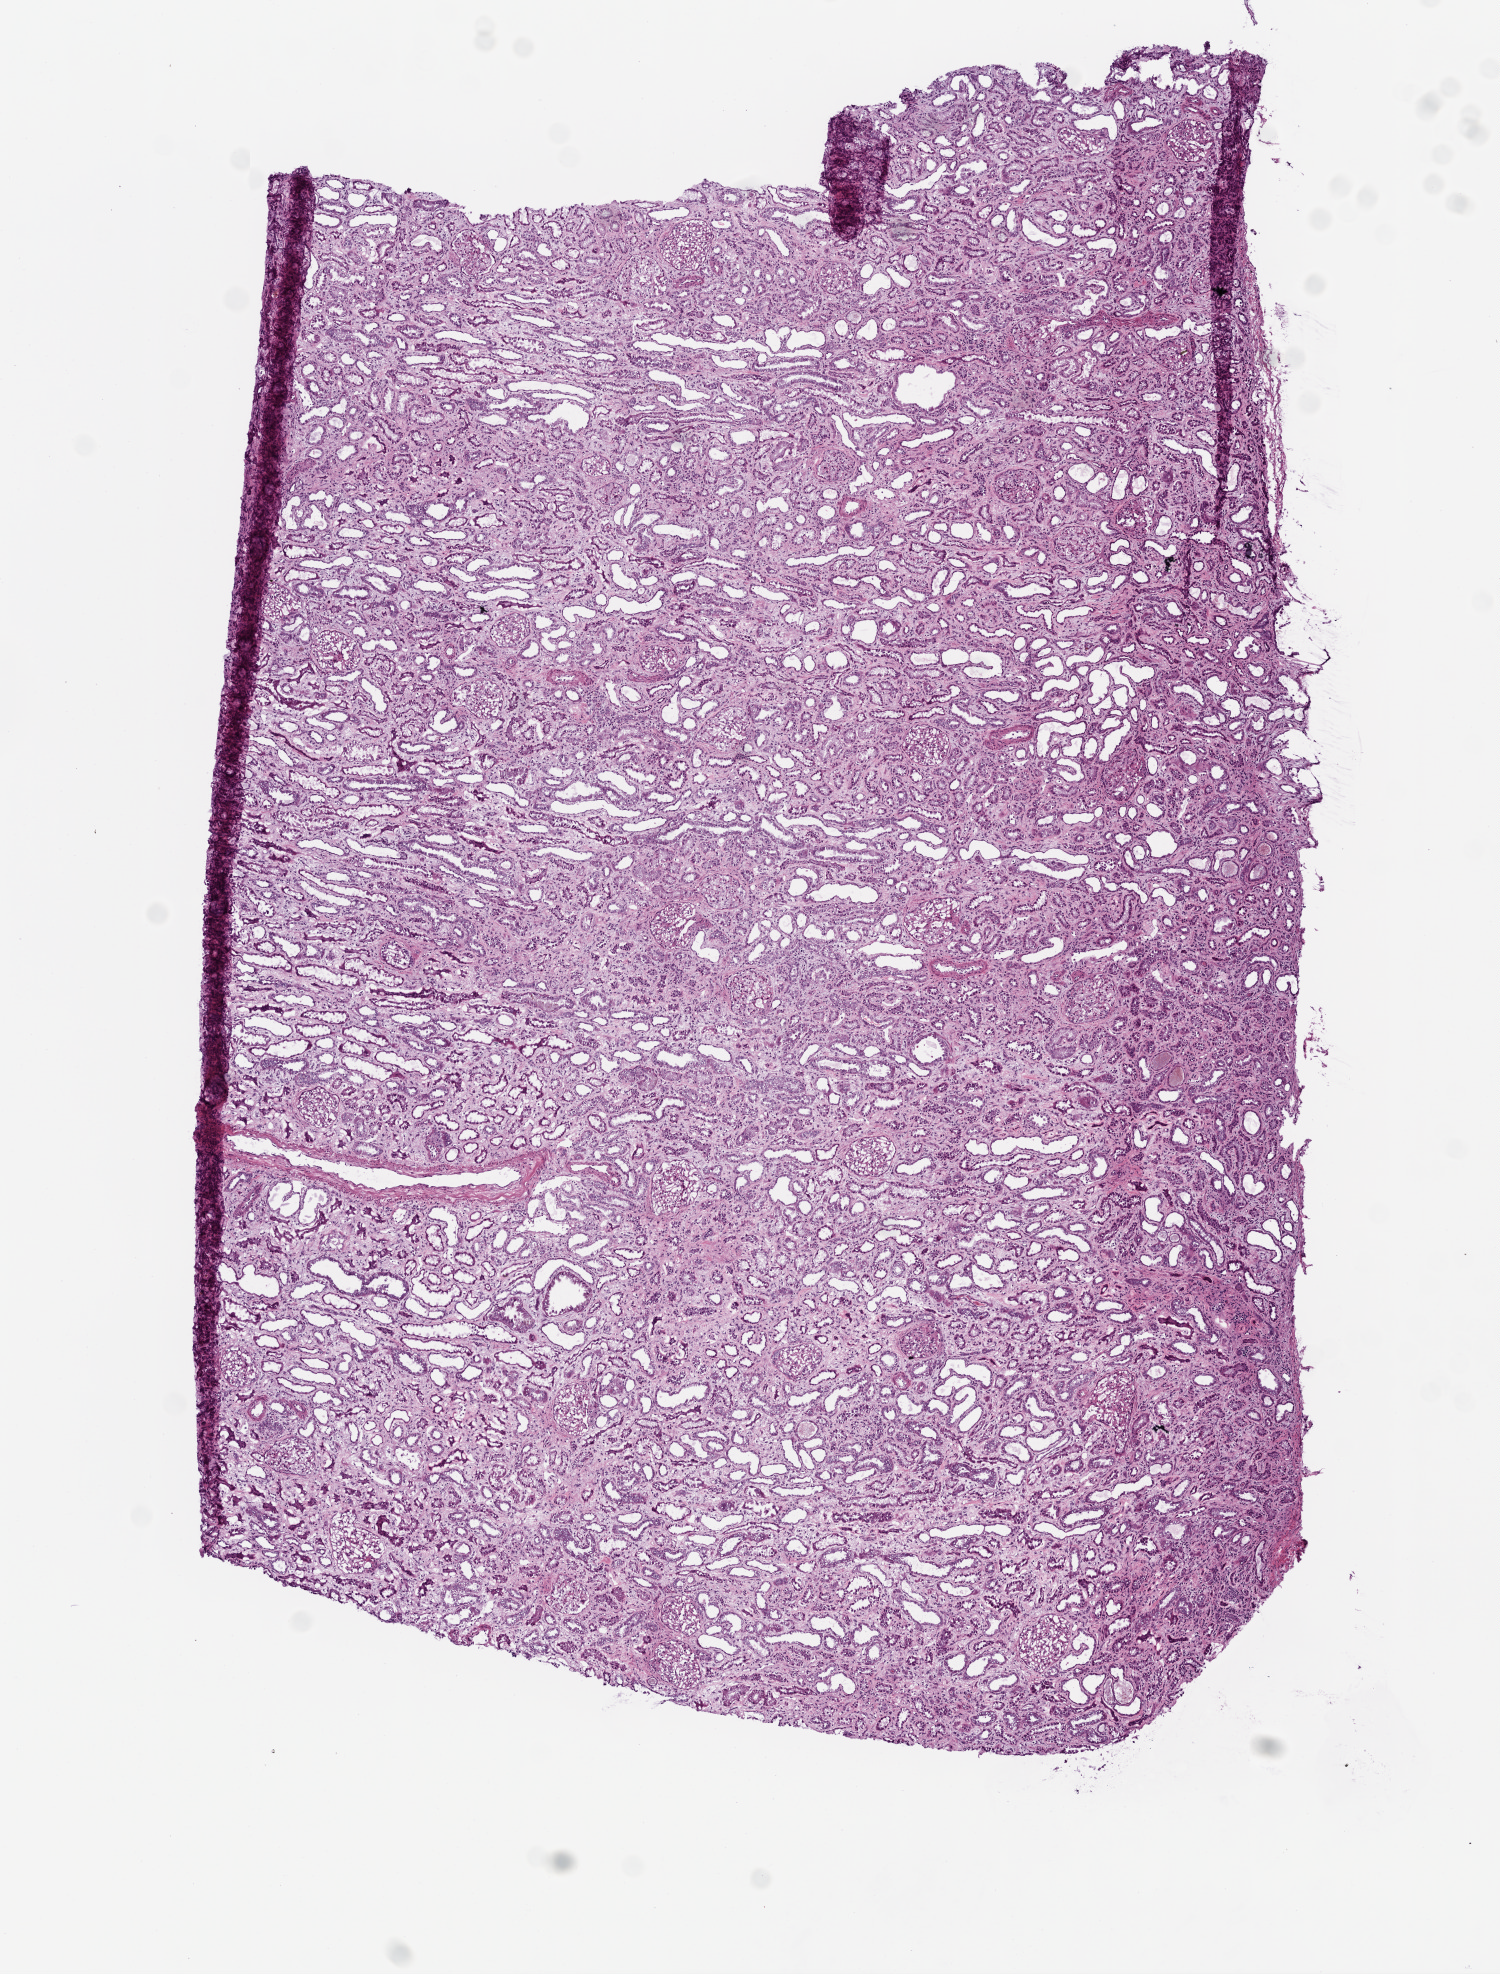
Whole-slide histology image, H&E-stained, a low-resolution overview of the entire scanned area, about 6.0 x 7.9 mm (from a 20x scan). Frozen section. Solid tissue normal (non-tumour tissue) sample from the kidney. Patient: male, age at initial diagnosis 56 years.
This section: solid tissue normal (non-tumour) sample from the same patient. Patient diagnosis: Clear cell adenocarcinoma, NOS.